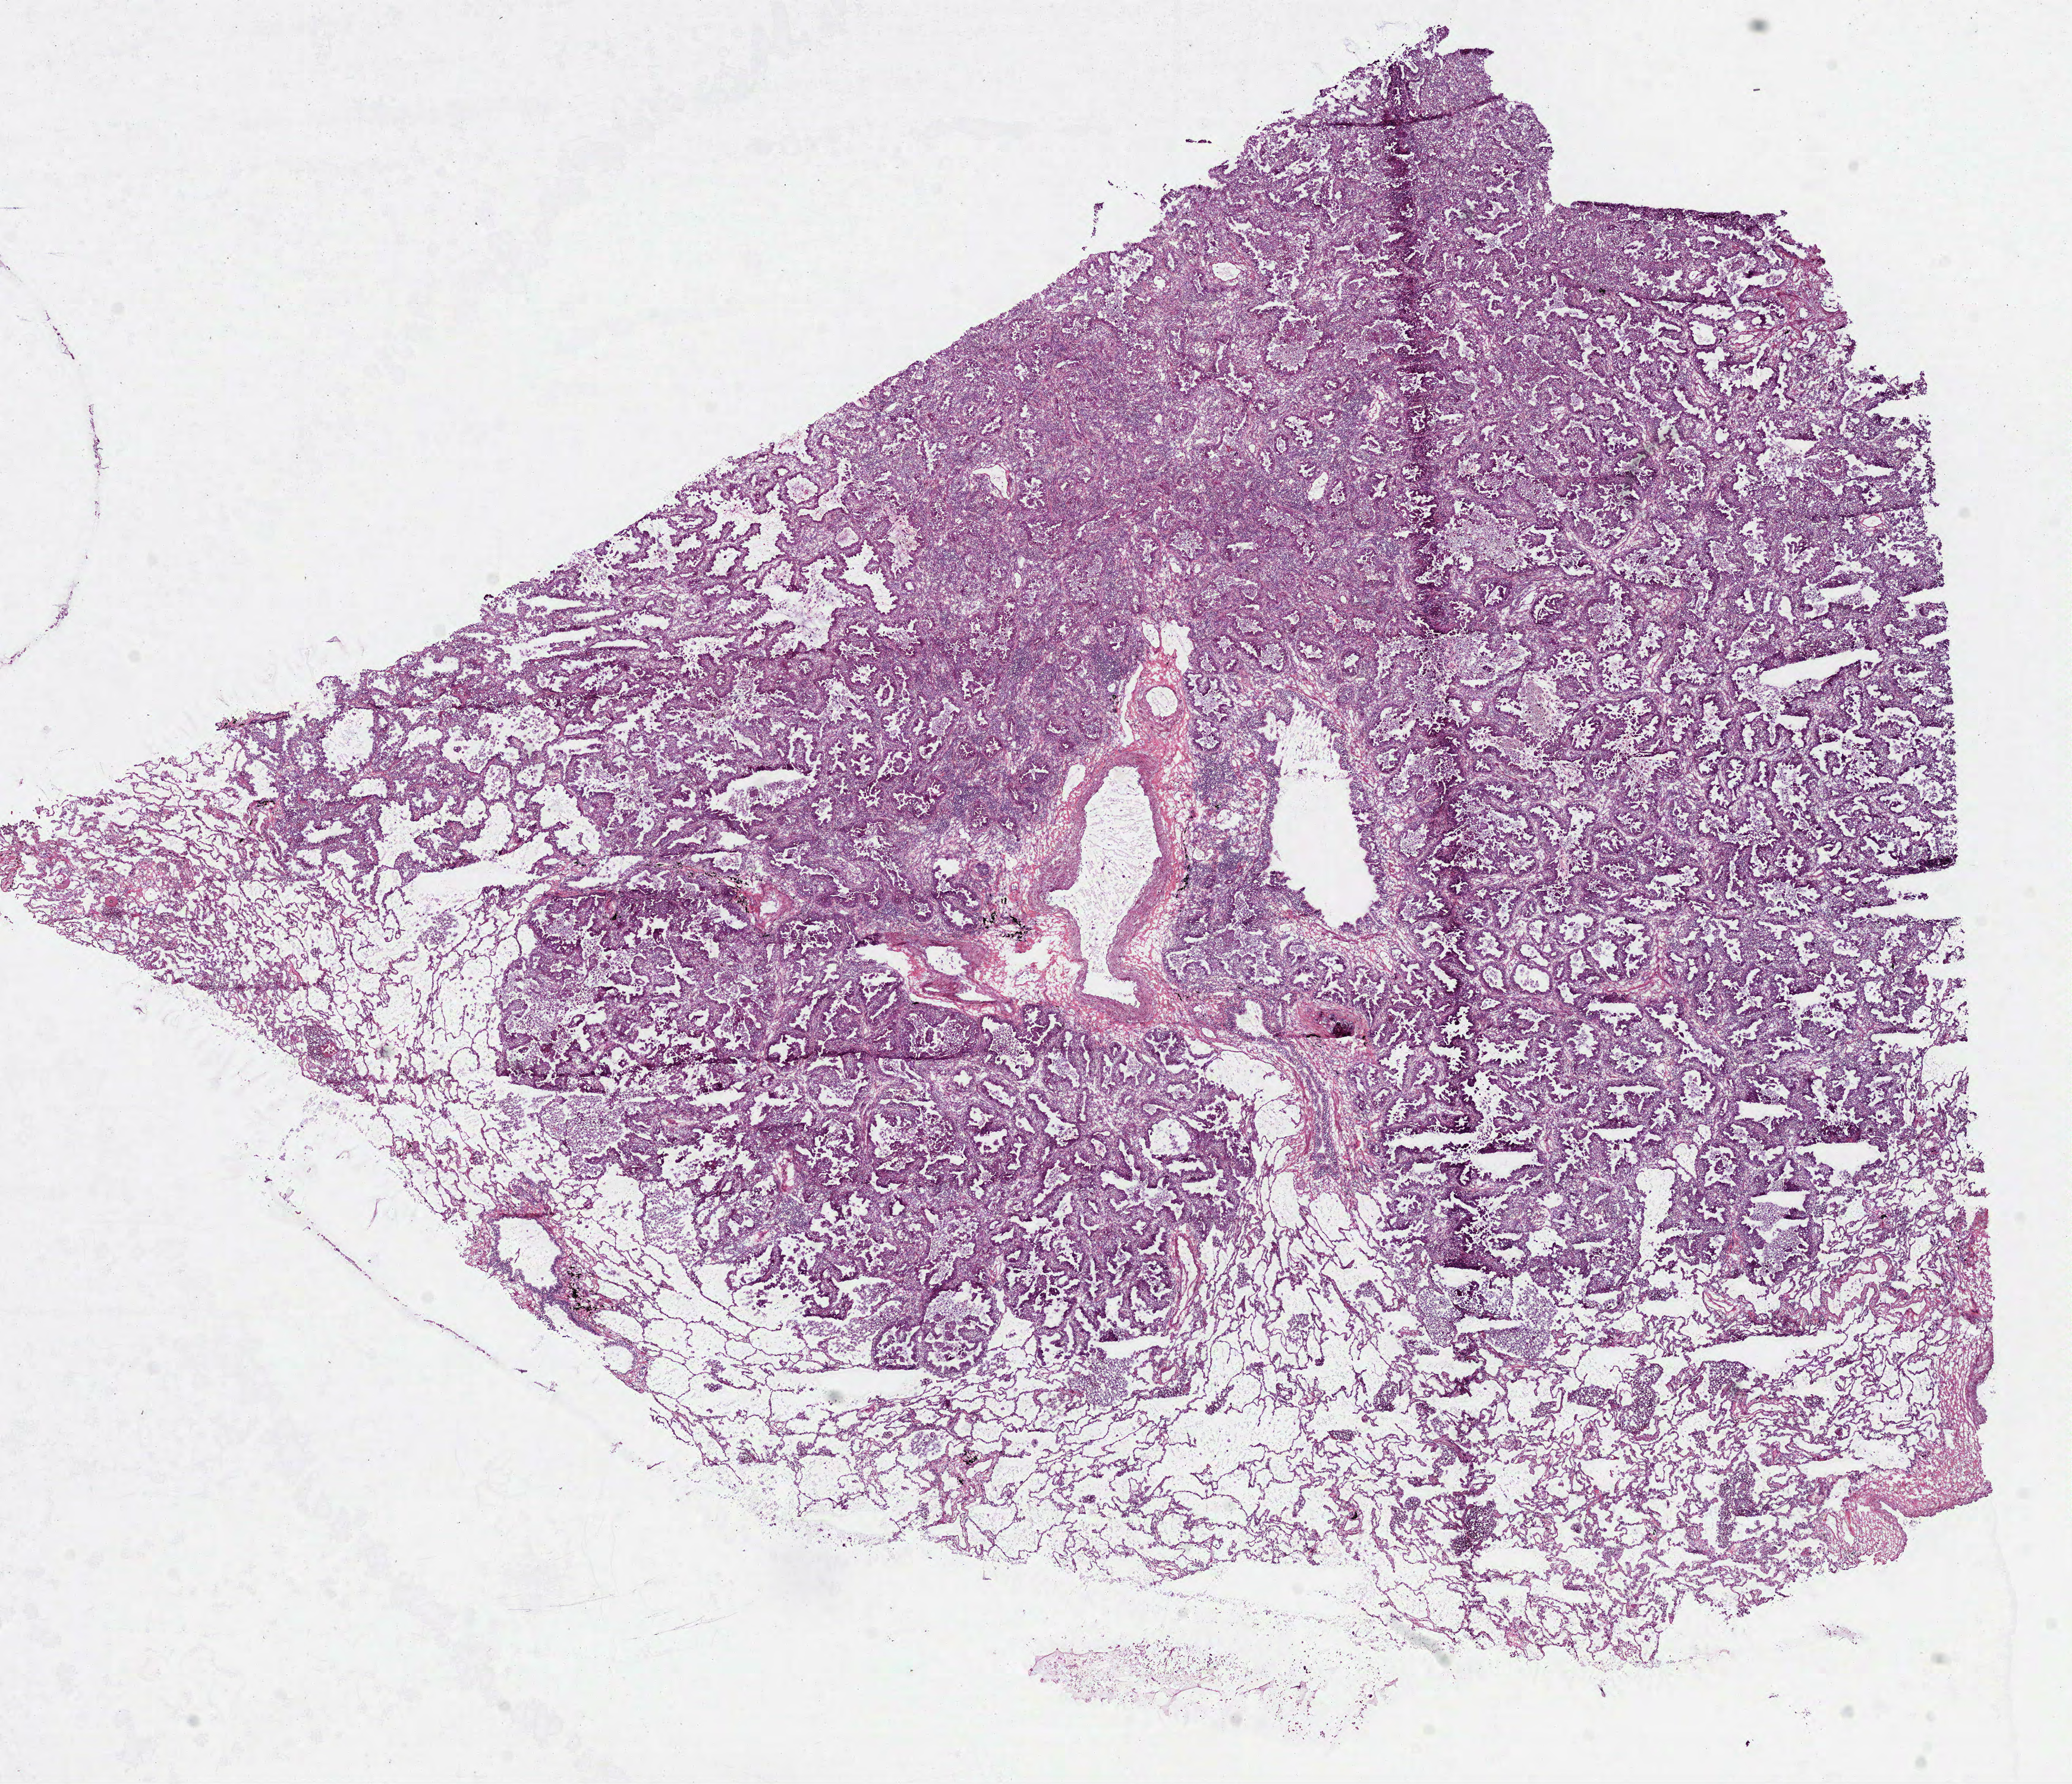
Whole-slide histology image, H&E-stained — a low-resolution overview of the entire scanned area, about 14.1 x 12.1 mm. Frozen section from the bottom of the tissue portion. Sample: primary tumour, lung. Female, age 84 years at initial diagnosis. Composition of this section per pathologist review: tumour cells 70%, tumour nuclei 70%, normal cells 15%, stromal cells 15%, necrosis 0%.
Diagnosis: Adenocarcinoma, NOS (upper lobe, lung). Laterality: right. AJCC pathologic stage: I (6th edition).